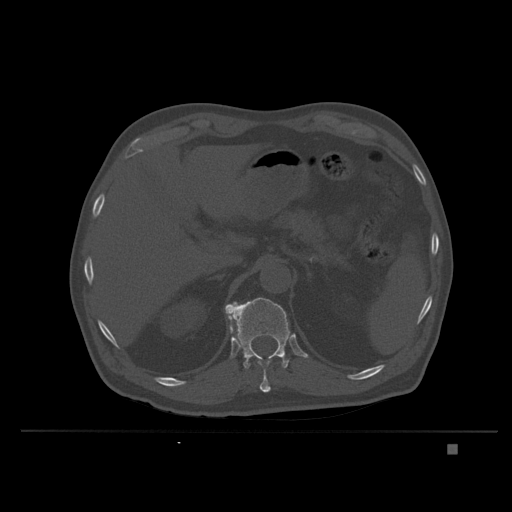
CT including the spine, one axial slice. Position 164 of 435 along the scan axis. Bone window (W 1800 / L 400 HU). 1.5 mm slice thickness. 512 × 512 image matrix, field of view 434 × 434 mm. Male patient, age 73 years. Case-level facts recorded for this patient, not image findings: primary cancer: skin.
Annotated regions visible in this slice (semi-automatically segmented with operator editing):
- T11 vertebra: bounding box (x1, y1, x2, y2) in pixels: (230, 327, 271, 392)
- T12 vertebra: (225, 297, 291, 368)